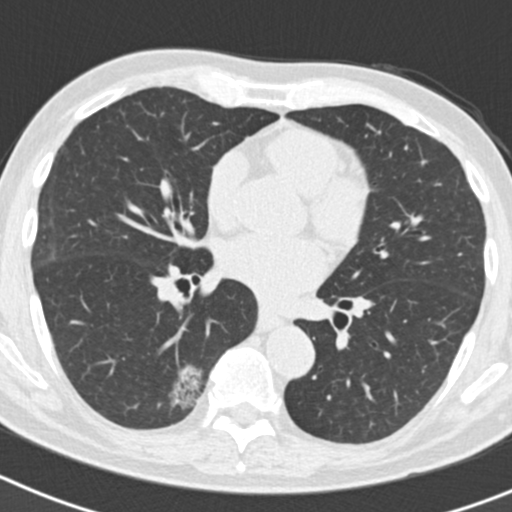
Chest CT (low-dose screening protocol), one axial image. Second annual screen. Lung window (W 1500 / L -600 HU). 2 mm slice thickness. Slice 91 of 186 in the series. Male, age 70 years at enrolment. Current smoker at enrolment.
Lesion marked by an expert reader, bounding box [x1, y1, x2, y2] px = [127, 362, 206, 430]. The screening reader recorded 5 non-calcified nodules or masses ≥4 mm on this exam; which of them this box marks is not recorded. Official screen result: positive, other. Participant outcome: lung cancer diagnosed 622 days after this screen (after the third annual screen) — bronchiolo-alveolar adenocarcinoma, NOS, right lower lobe, poorly differentiated (G3), stage IB (AJCC 6th edition), 30 mm at pathology.